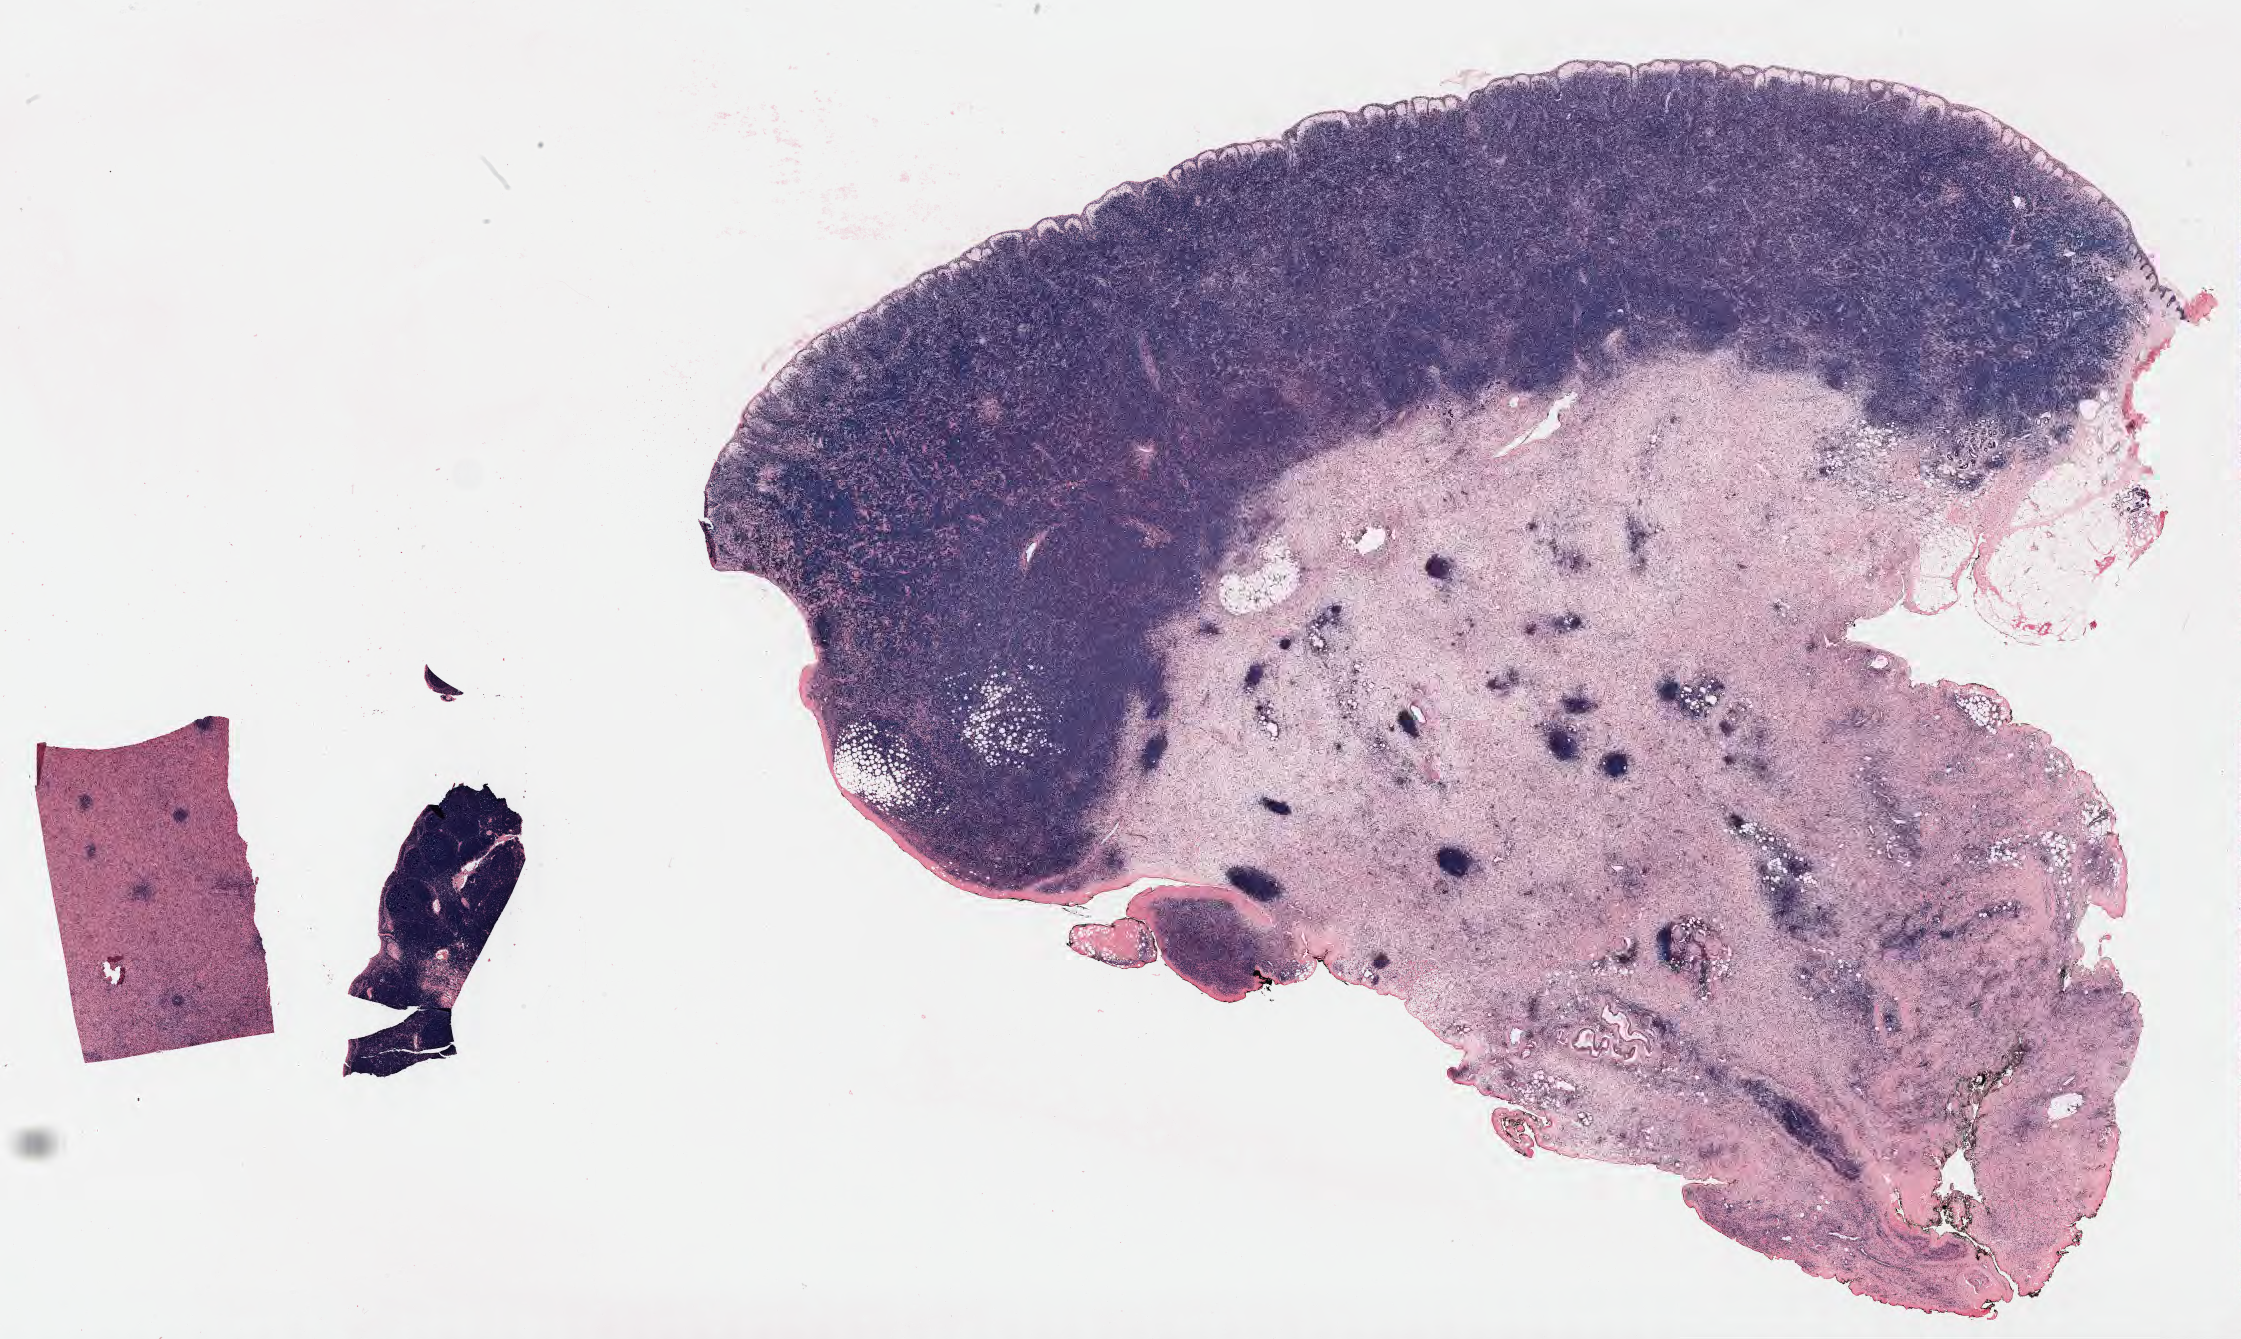
Whole-slide image; stain recorded as Iodonitrotetrazolium, whole scanned area (about 36.2 x 21.6 mm) shown as a low-resolution overview; specimen: tumor tissue; site: lymph node. Patient male; aged 52.
Diagnosis: Diffuse large B-cell lymphoma, NOS.